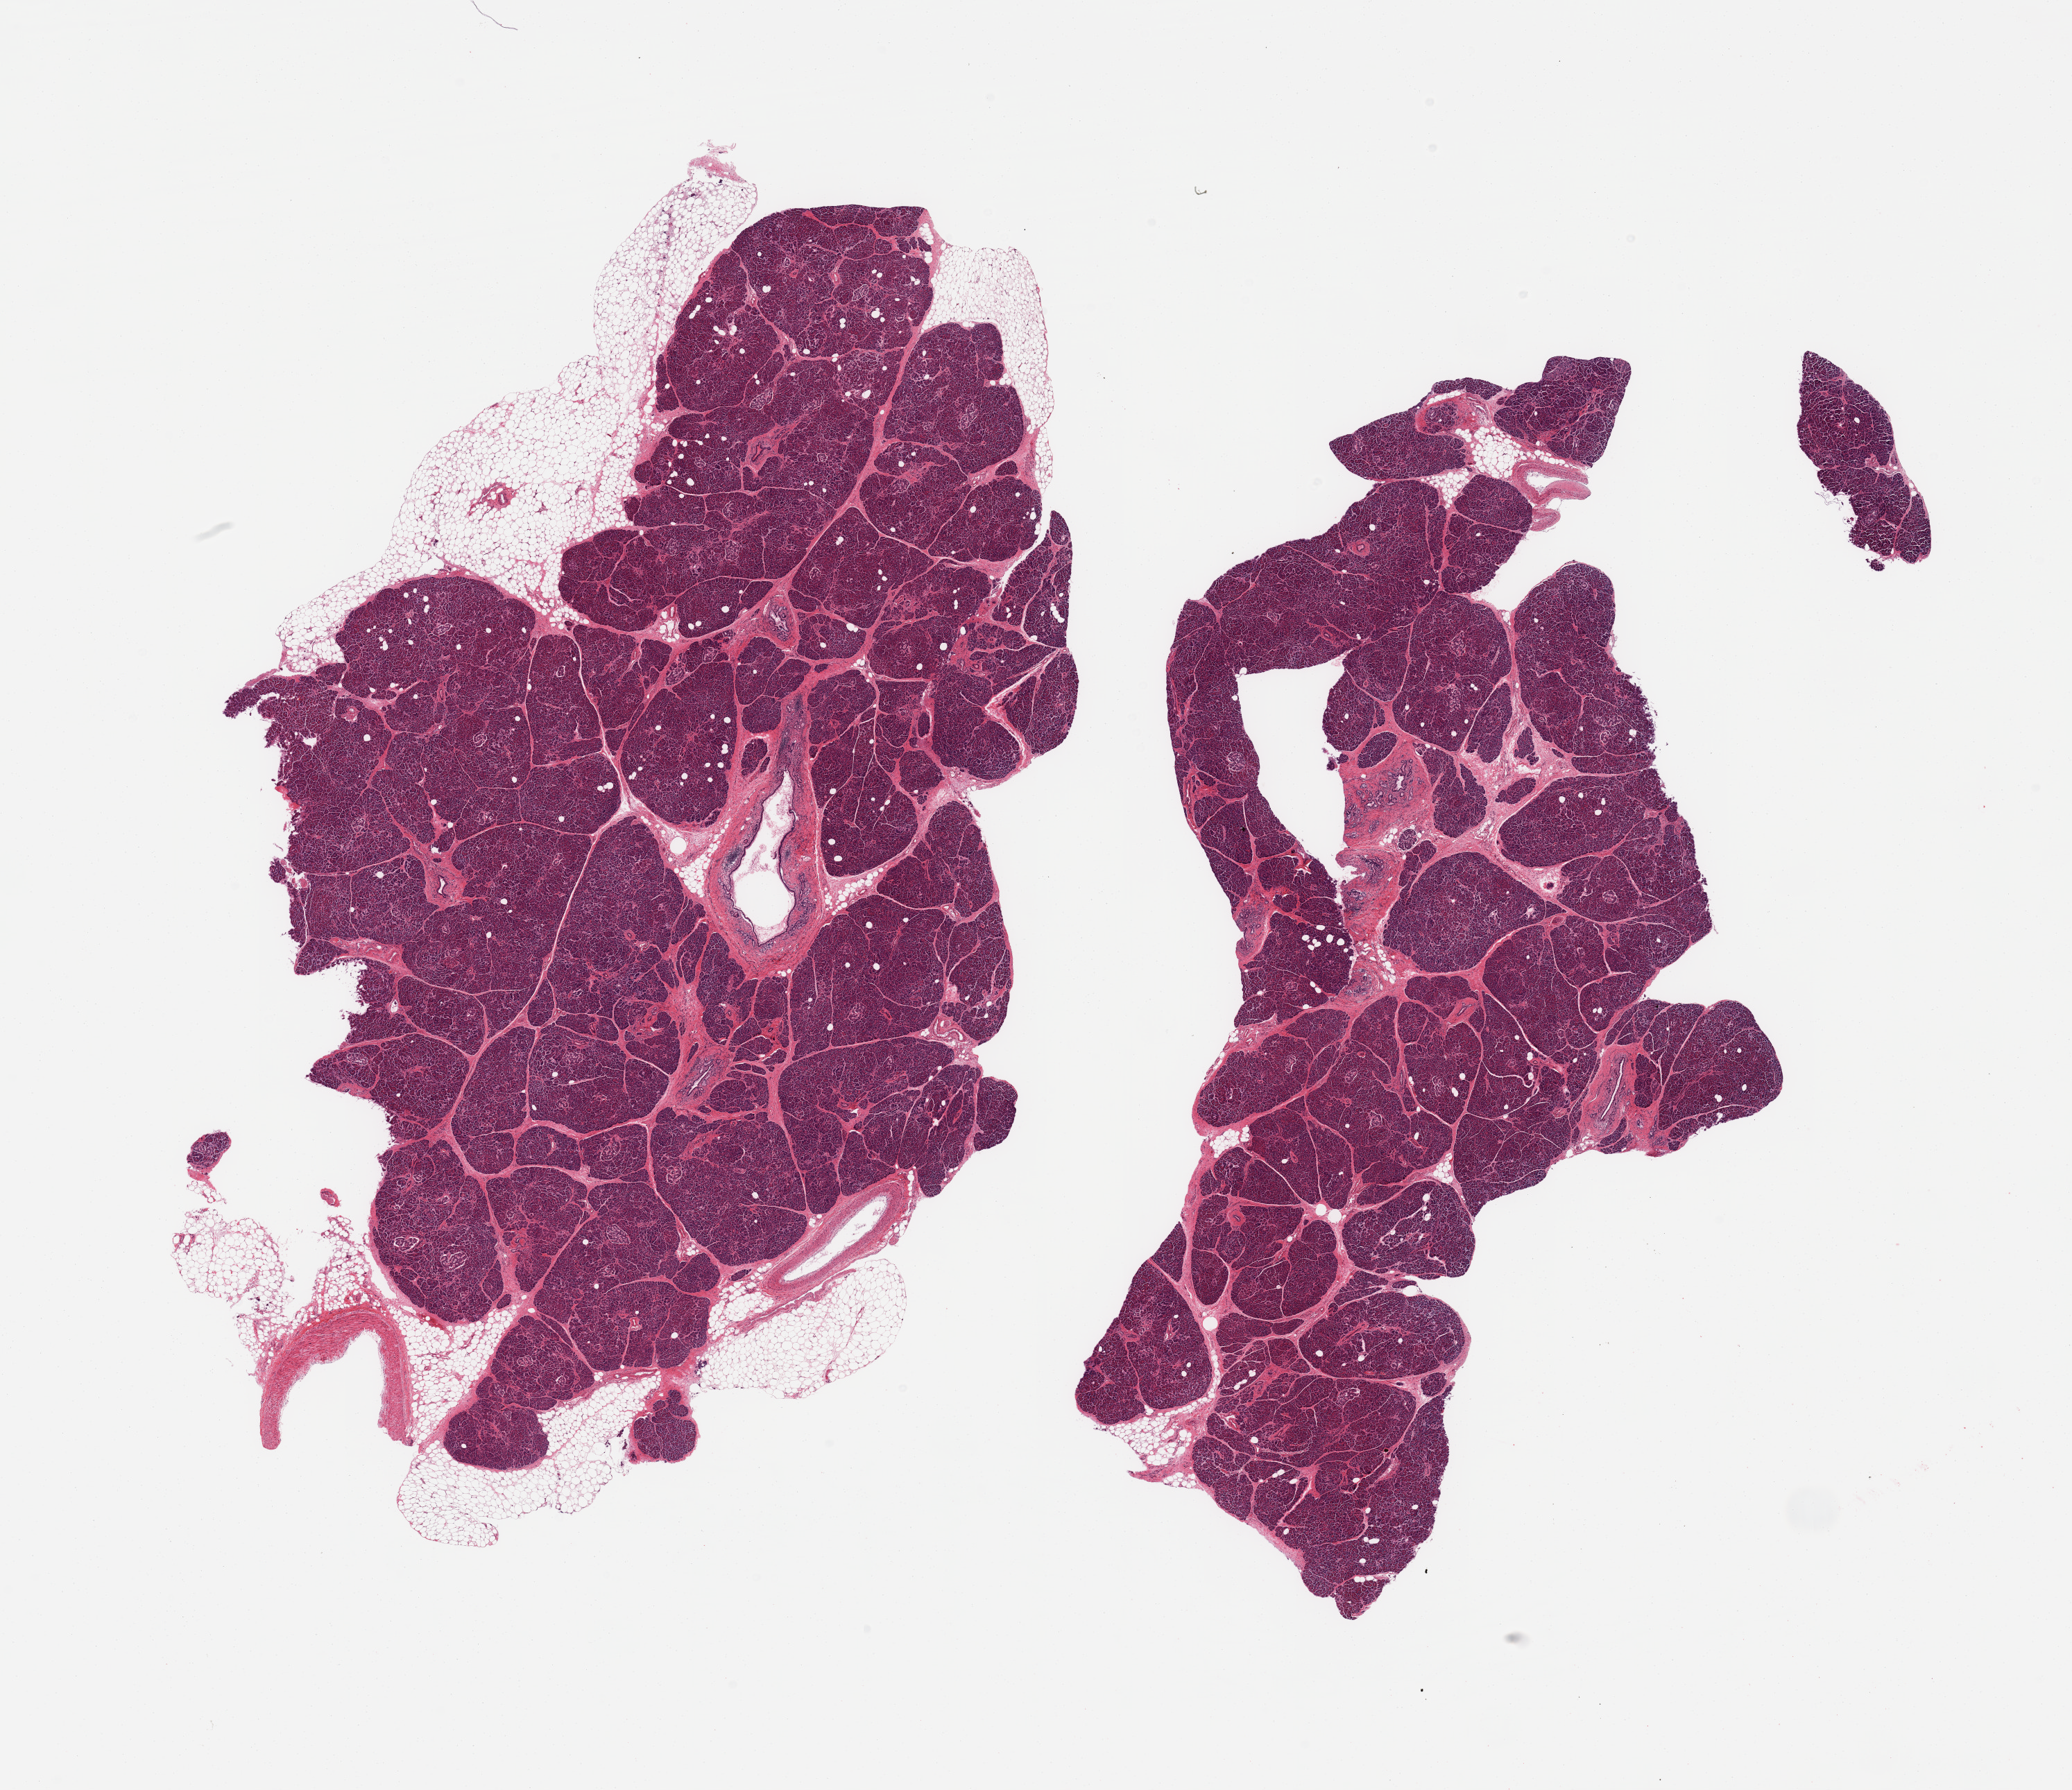
Whole-slide image, haematoxylin and eosin stain, a low-resolution overview of the entire scanned area, about 23.6 x 20.4 mm (slide scanned at 20x); PAXgene-fixed, paraffin-embedded tissue; sampled site (target tissue): pancreas; donor tissue sample.
- reviewer comment on this tissue sample: 2 pieces; 1 piece includes ~20% external fat, mild fibrosis, islets well visualized, PanIN-1A, mild periductal chronic inflammation